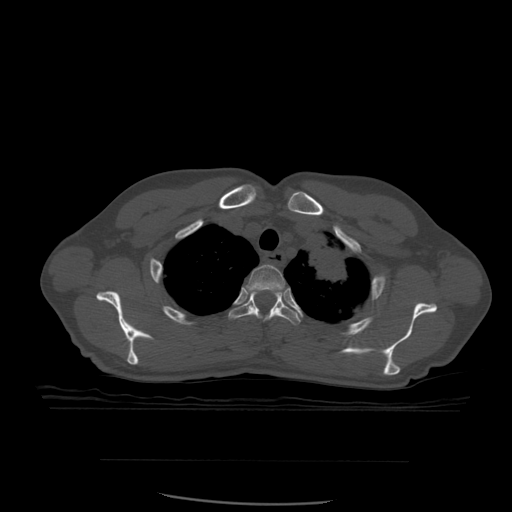
CT including the spine, one axial slice. Bone window (W 1800 / L 400 HU). 1.25 mm slice thickness. 512 × 512 image matrix, field of view 392 × 392 mm. Patient age 48 years. From the clinical record (not read from this slice): primary cancer: lung; vertebrae with lytic lesions (as recorded): T11.
Structures marked on this image (semi-automatically segmented with operator editing):
- T2 vertebra: bounding box <247,265,286,312> (left, top, right, bottom; pixels)
- T3 vertebra: <229,290,301,325>